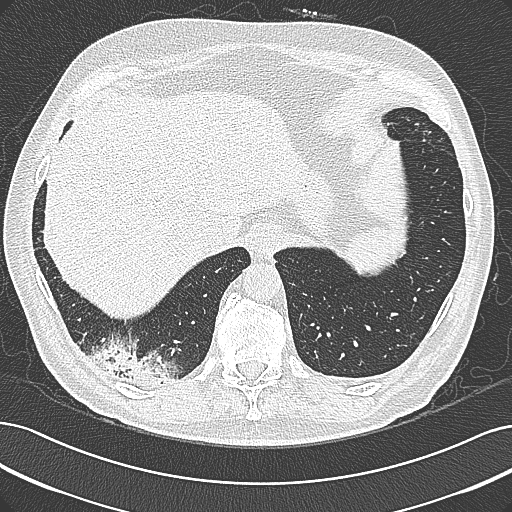
Chest CT (low-dose screening protocol), one axial image, baseline screening round, lung window (W 1500 / L -600 HU), 1 mm slice thickness. Male, age 68 years at enrolment. Former smoker at enrolment.
• Expert reader's lesion annotation, bounding box (x1, y1, x2, y2) in pixels: (95, 338, 190, 399).
• Screening reader's record for this exam: no non-calcified nodule ≥4 mm recorded.
• Later outcome: lung cancer diagnosed 154 days after this screen — mucinous adenocarcinoma, right lower lobe, well differentiated (G1), stage IB (AJCC 6th edition), 50 mm at pathology.